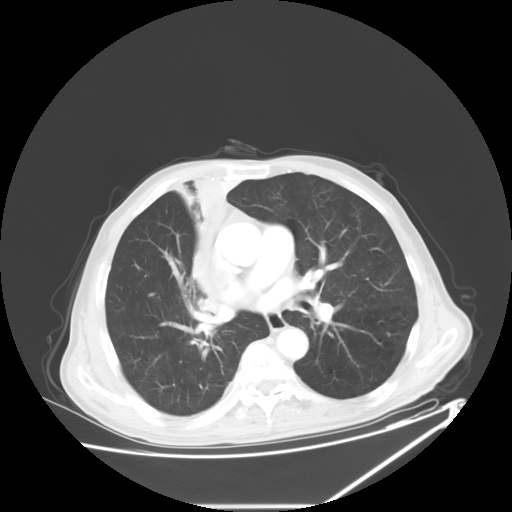
Chest CT, one axial slice. Reconstruction kernel STANDARD. 120 kVp. Lung window (W 1500 / L -600 HU). 5 mm slice thickness. 512 × 512 image matrix. Male patient, age 73 years. From the clinical record (not read from this slice): clinical TNM (as recorded): T2a N1 M0.
Annotated regions visible in this slice (rectangle marked by the reading radiologist):
- lung tumour (recorded histology: squamous cell carcinoma): bounding box <175,165,245,310> (left, top, right, bottom; pixels)